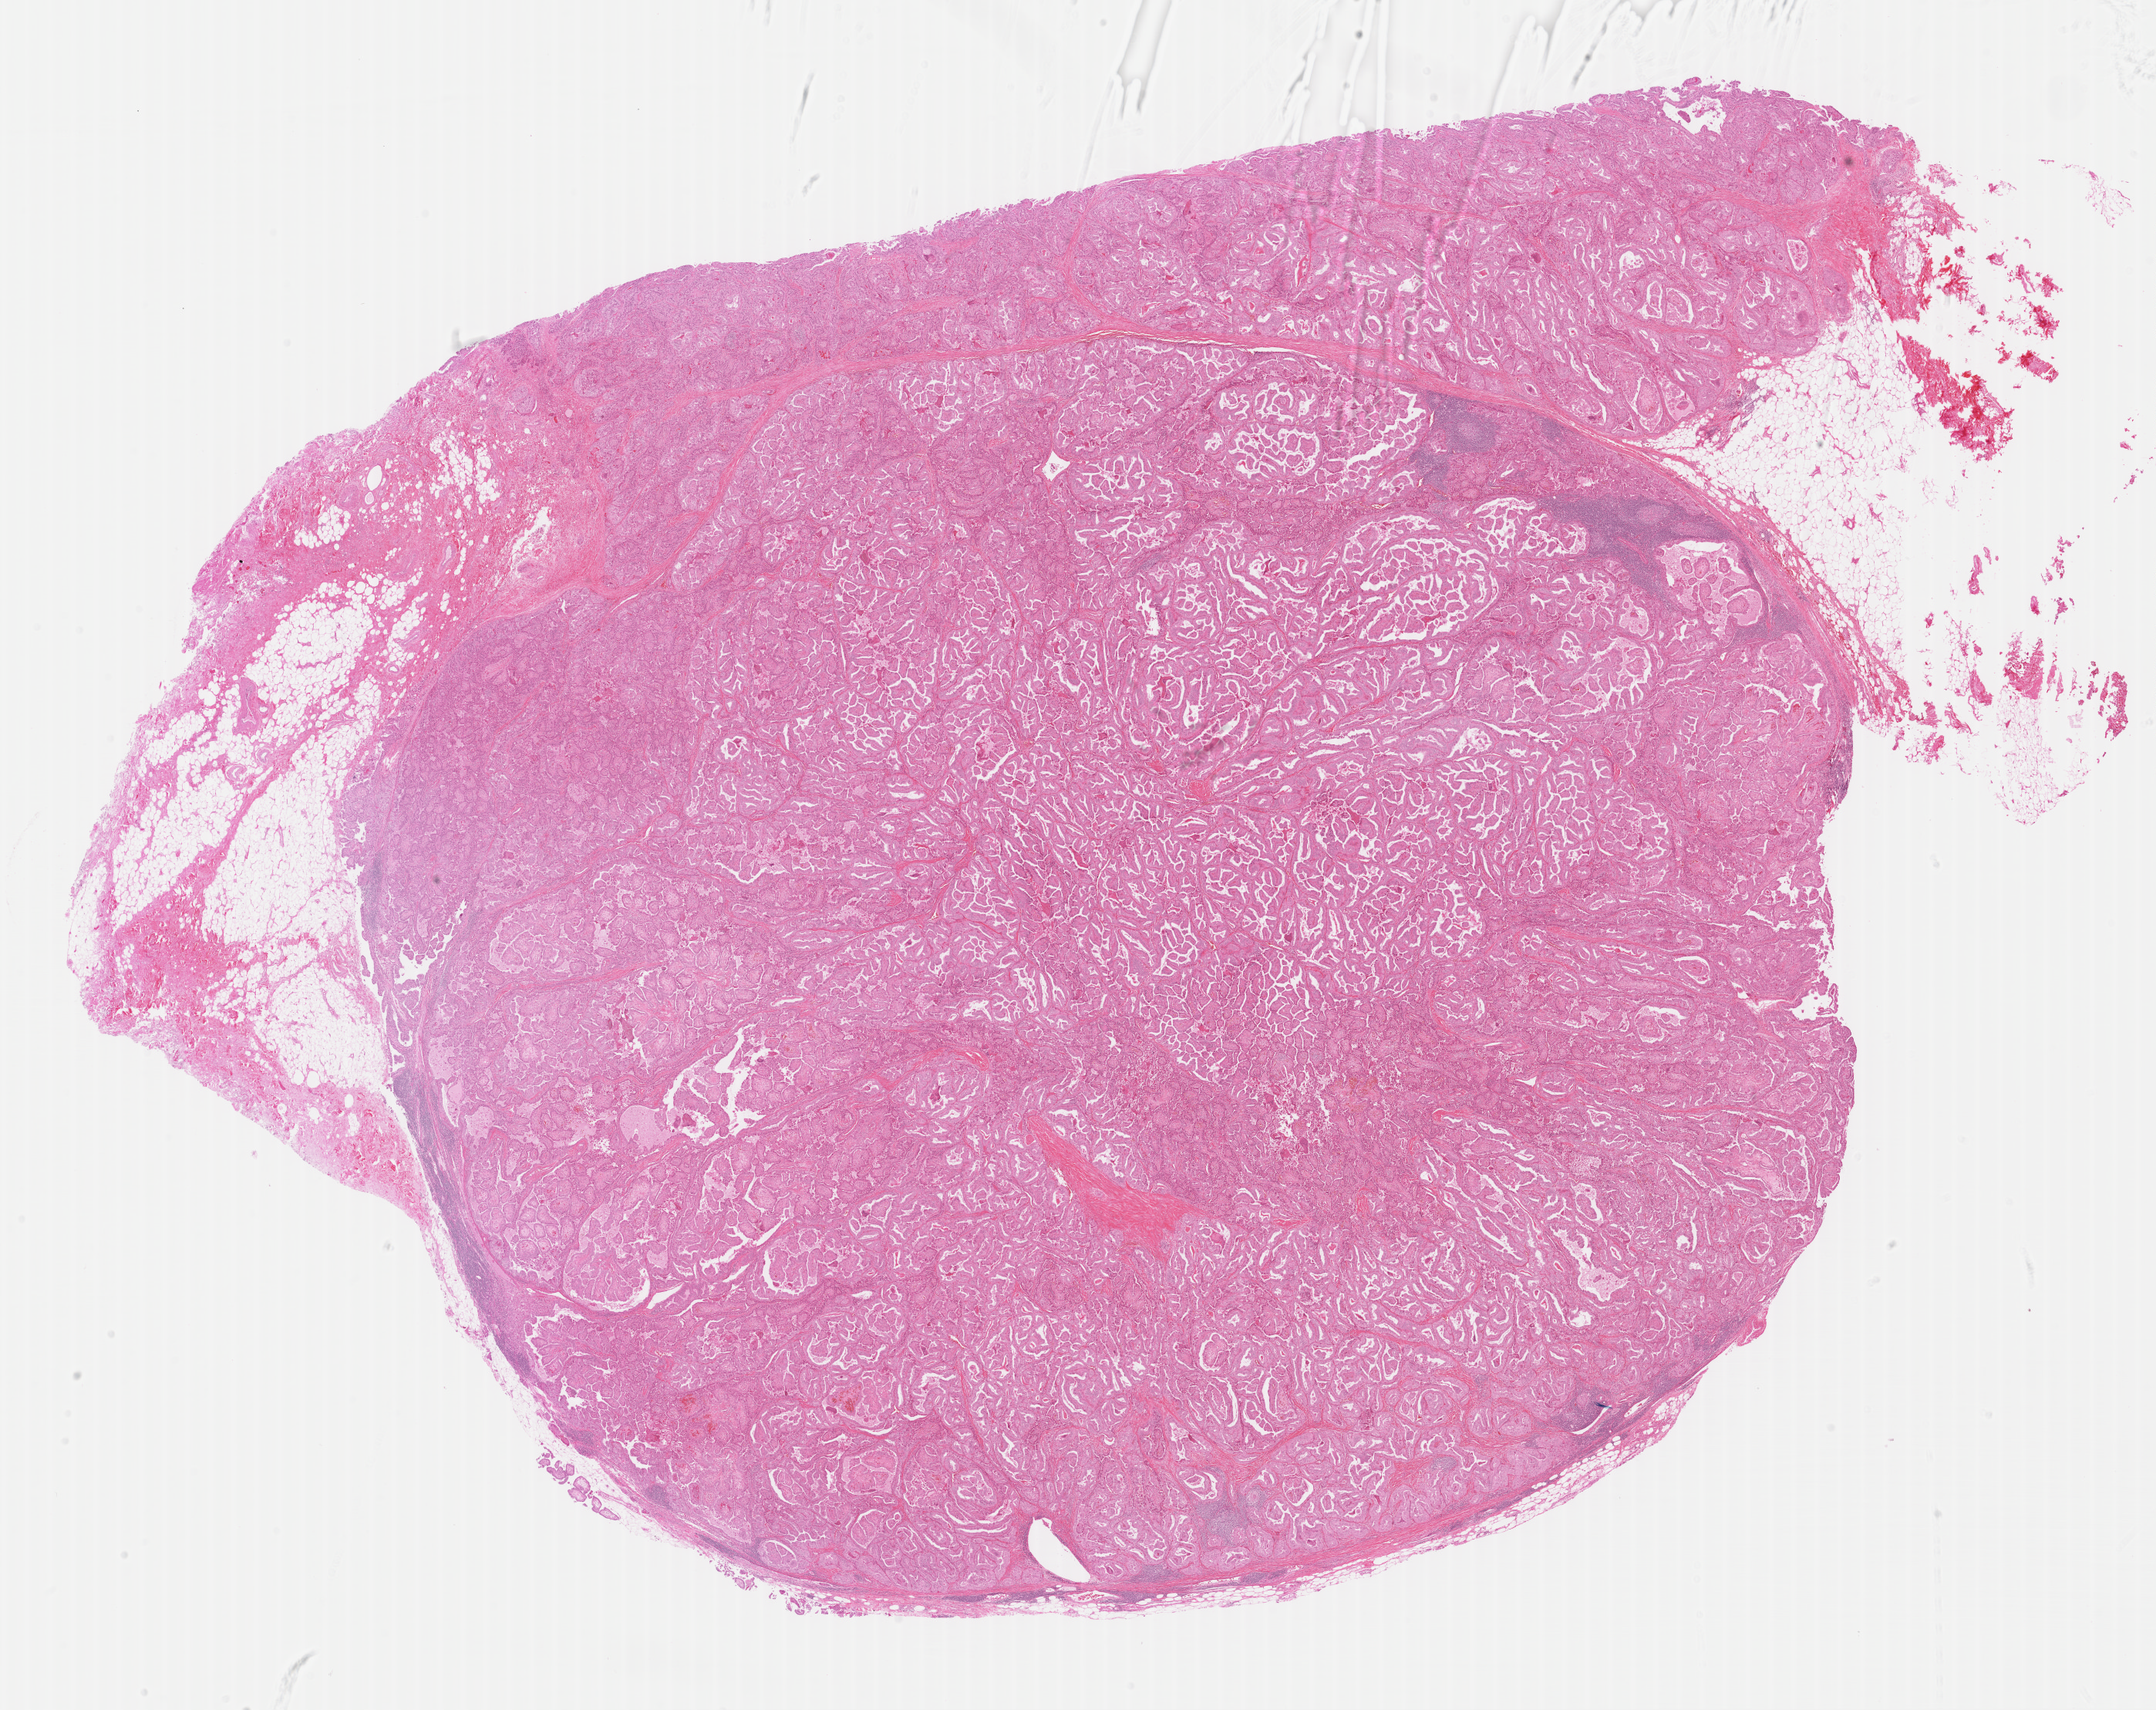
Hematoxylin and eosin (H&E) stained whole-slide image, shown as a low-resolution overview of the whole scanned area (about 22.1 x 17.5 mm, from a 40x scan). Formalin-fixed paraffin-embedded (FFPE) diagnostic section. Primary tumour sample from the thyroid. Female, age 78 years at initial diagnosis.
* TNM: T4a N1a M0
* histologic diagnosis: Papillary adenocarcinoma, NOS (thyroid gland)
* AJCC pathologic stage: IVA (6th edition)
* lymph nodes positive (case pathology): 2 of 17 examined